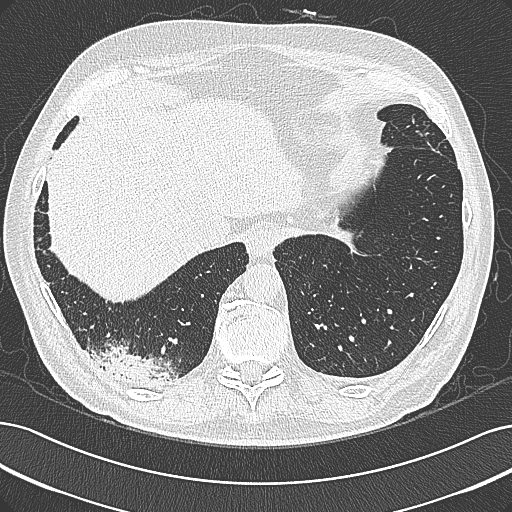
Axial slice from a low-dose chest CT screening exam; first (baseline) screen; lung window (W 1500 / L -600 HU); 512 × 512 image matrix. Male, age 68 years at enrolment. Former smoker at enrolment.
- Expert reader's lesion annotation, bounding box <96,339,188,400> (left, top, right, bottom; pixels).
- Screening reader's record for this exam: no non-calcified nodule ≥4 mm recorded.
- Lung cancer was diagnosed 154 days after this screen: mucinous adenocarcinoma, right lower lobe, well differentiated (G1), stage IB (AJCC 6th edition), 50 mm at pathology.